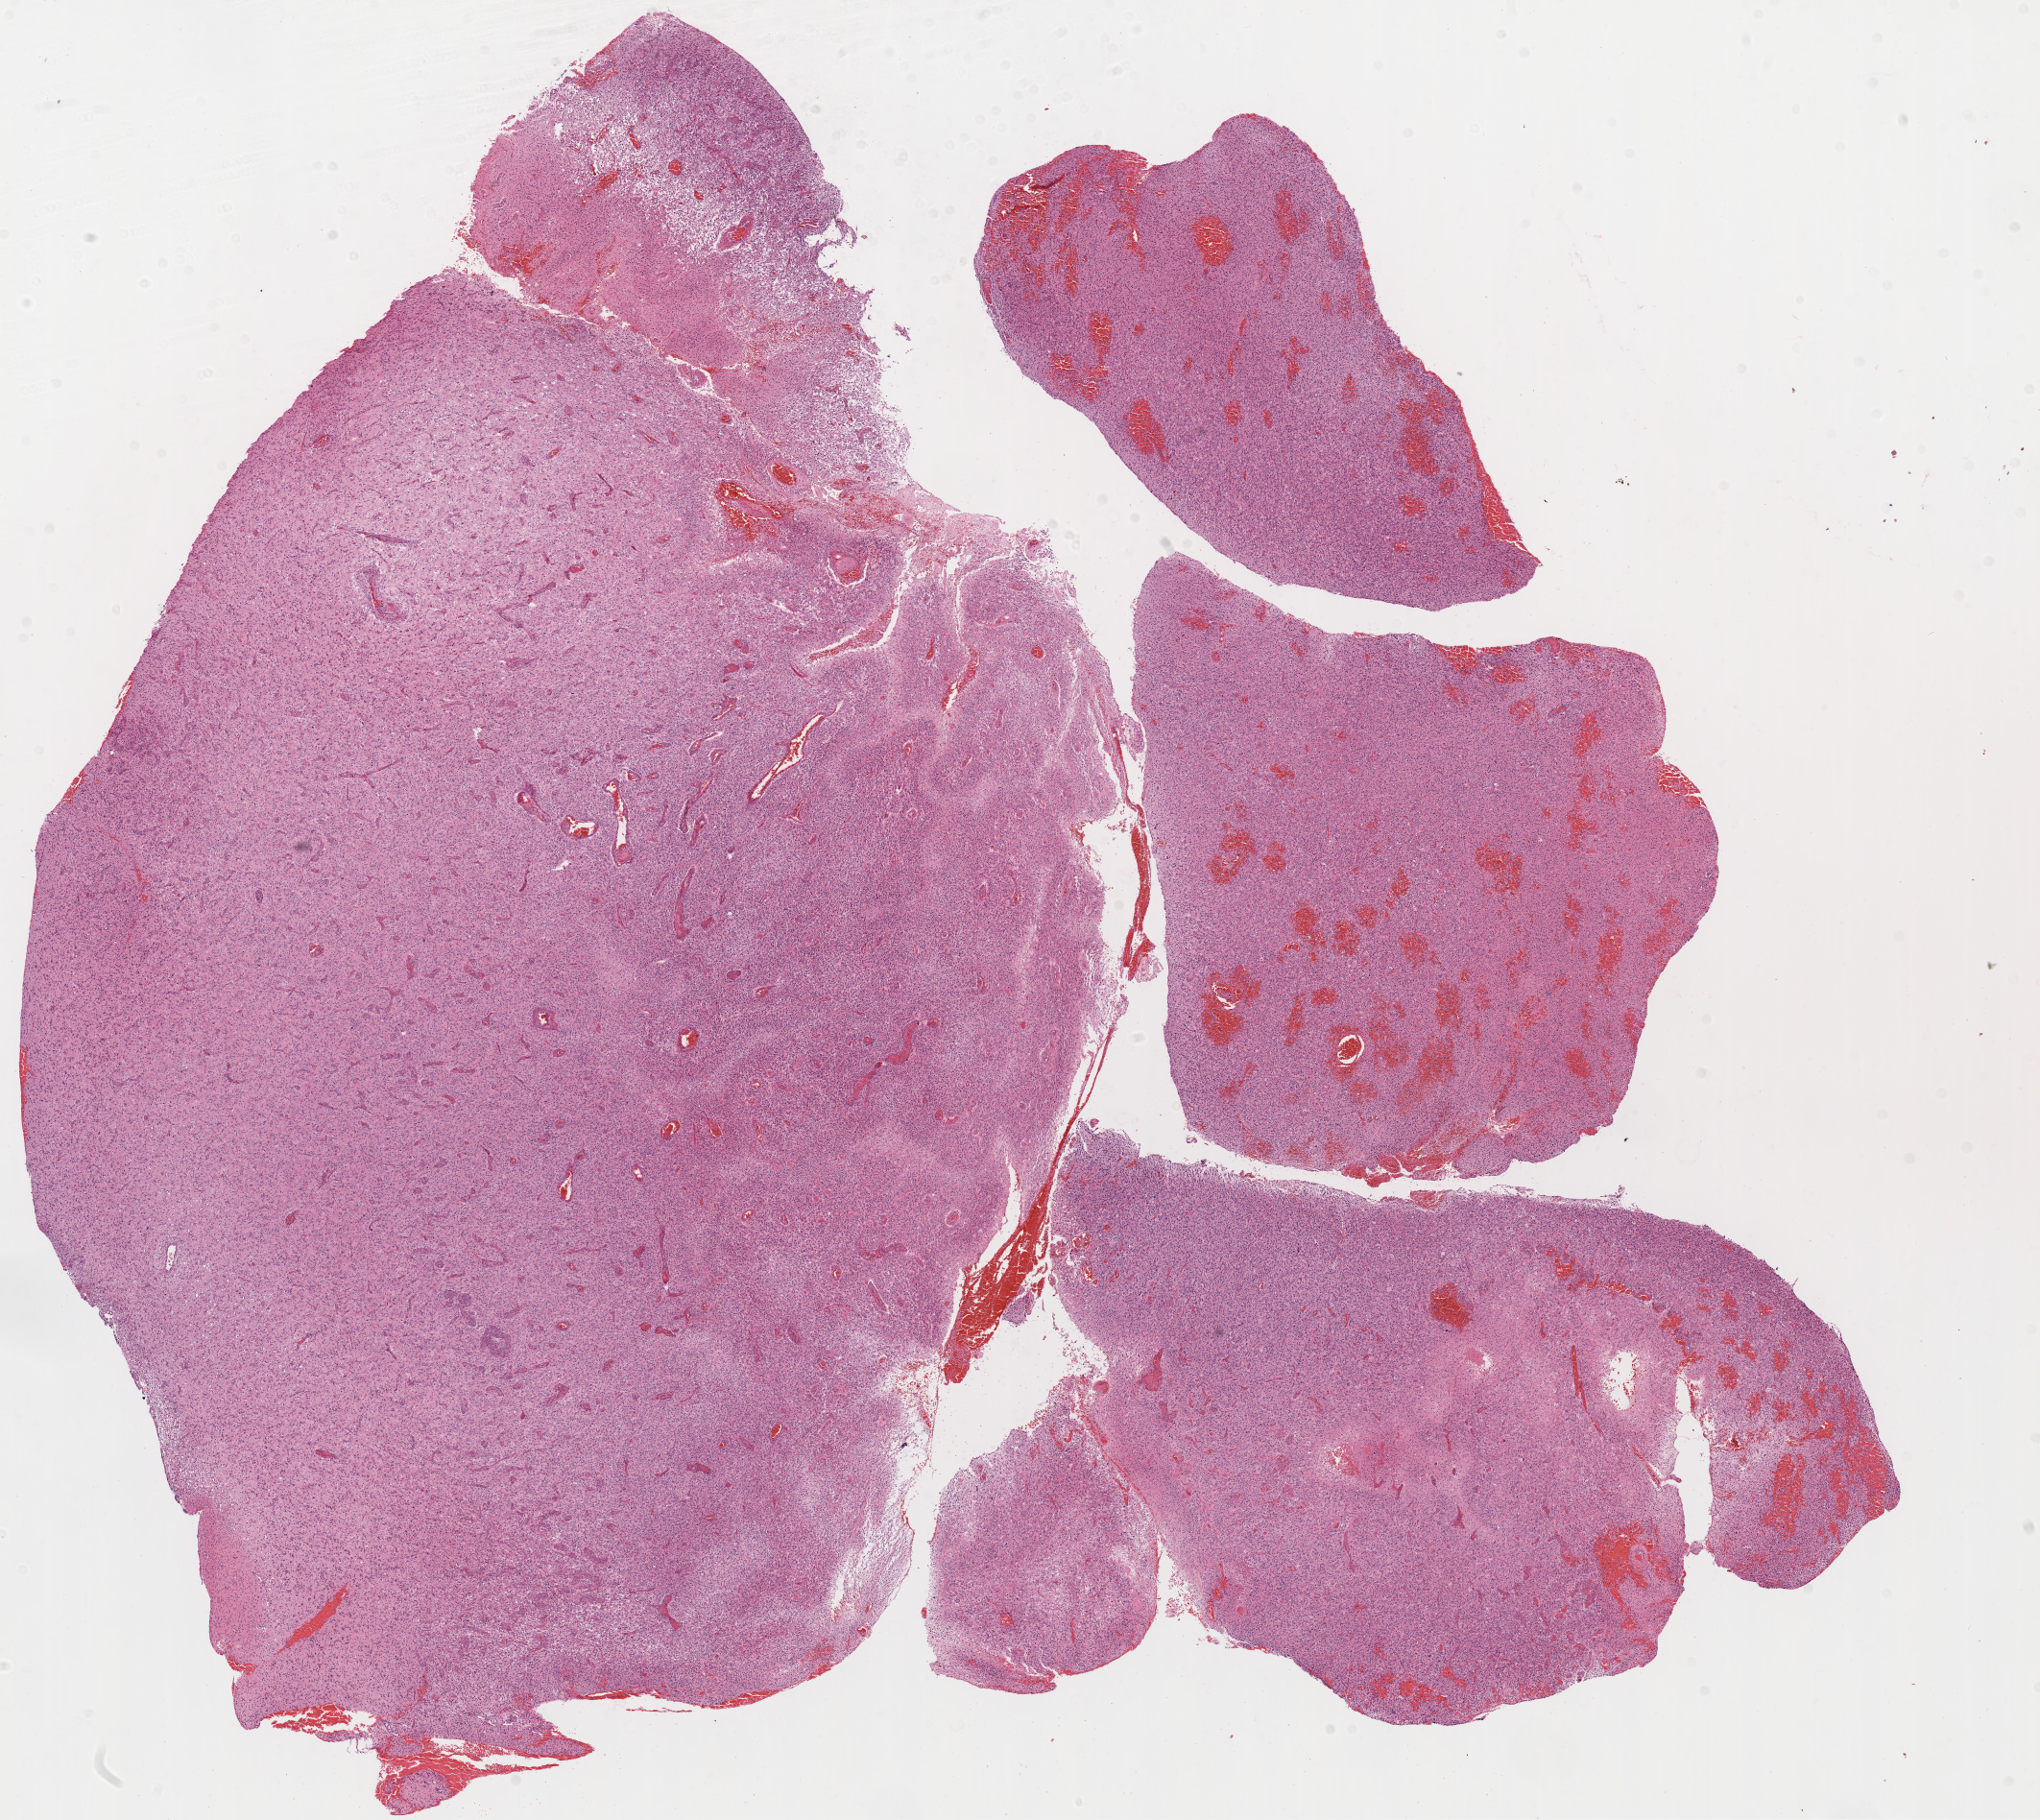
Digitized Hematoxylin and eosin (H&E) stained tissue section (whole slide) — shown as a low-resolution overview of the whole scanned area (about 17.1 x 15.2 mm, from a 20x scan), formalin-fixed paraffin-embedded (FFPE) diagnostic section, primary tumour sample from the brain. Patient: male, age at initial diagnosis 67 years.
* histologic diagnosis: Glioblastoma